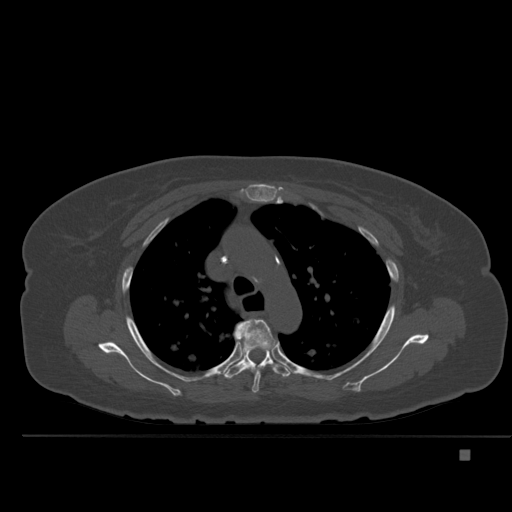
CT including the spine, one axial slice. Position 360 of 477 along the scan axis. Bone window (W 1800 / L 400 HU). 512 × 512 image matrix, field of view 422 × 422 mm. Female patient, age 74 years. From the clinical record (not read from this slice): primary cancer: colon.
Structures marked on this image (semi-automatic segmentation, software-assisted and operator-edited):
- T4 vertebra: box from (x=235, y=318) to (x=276, y=393) px
- T5 vertebra: (x=224, y=325)–(x=291, y=379)